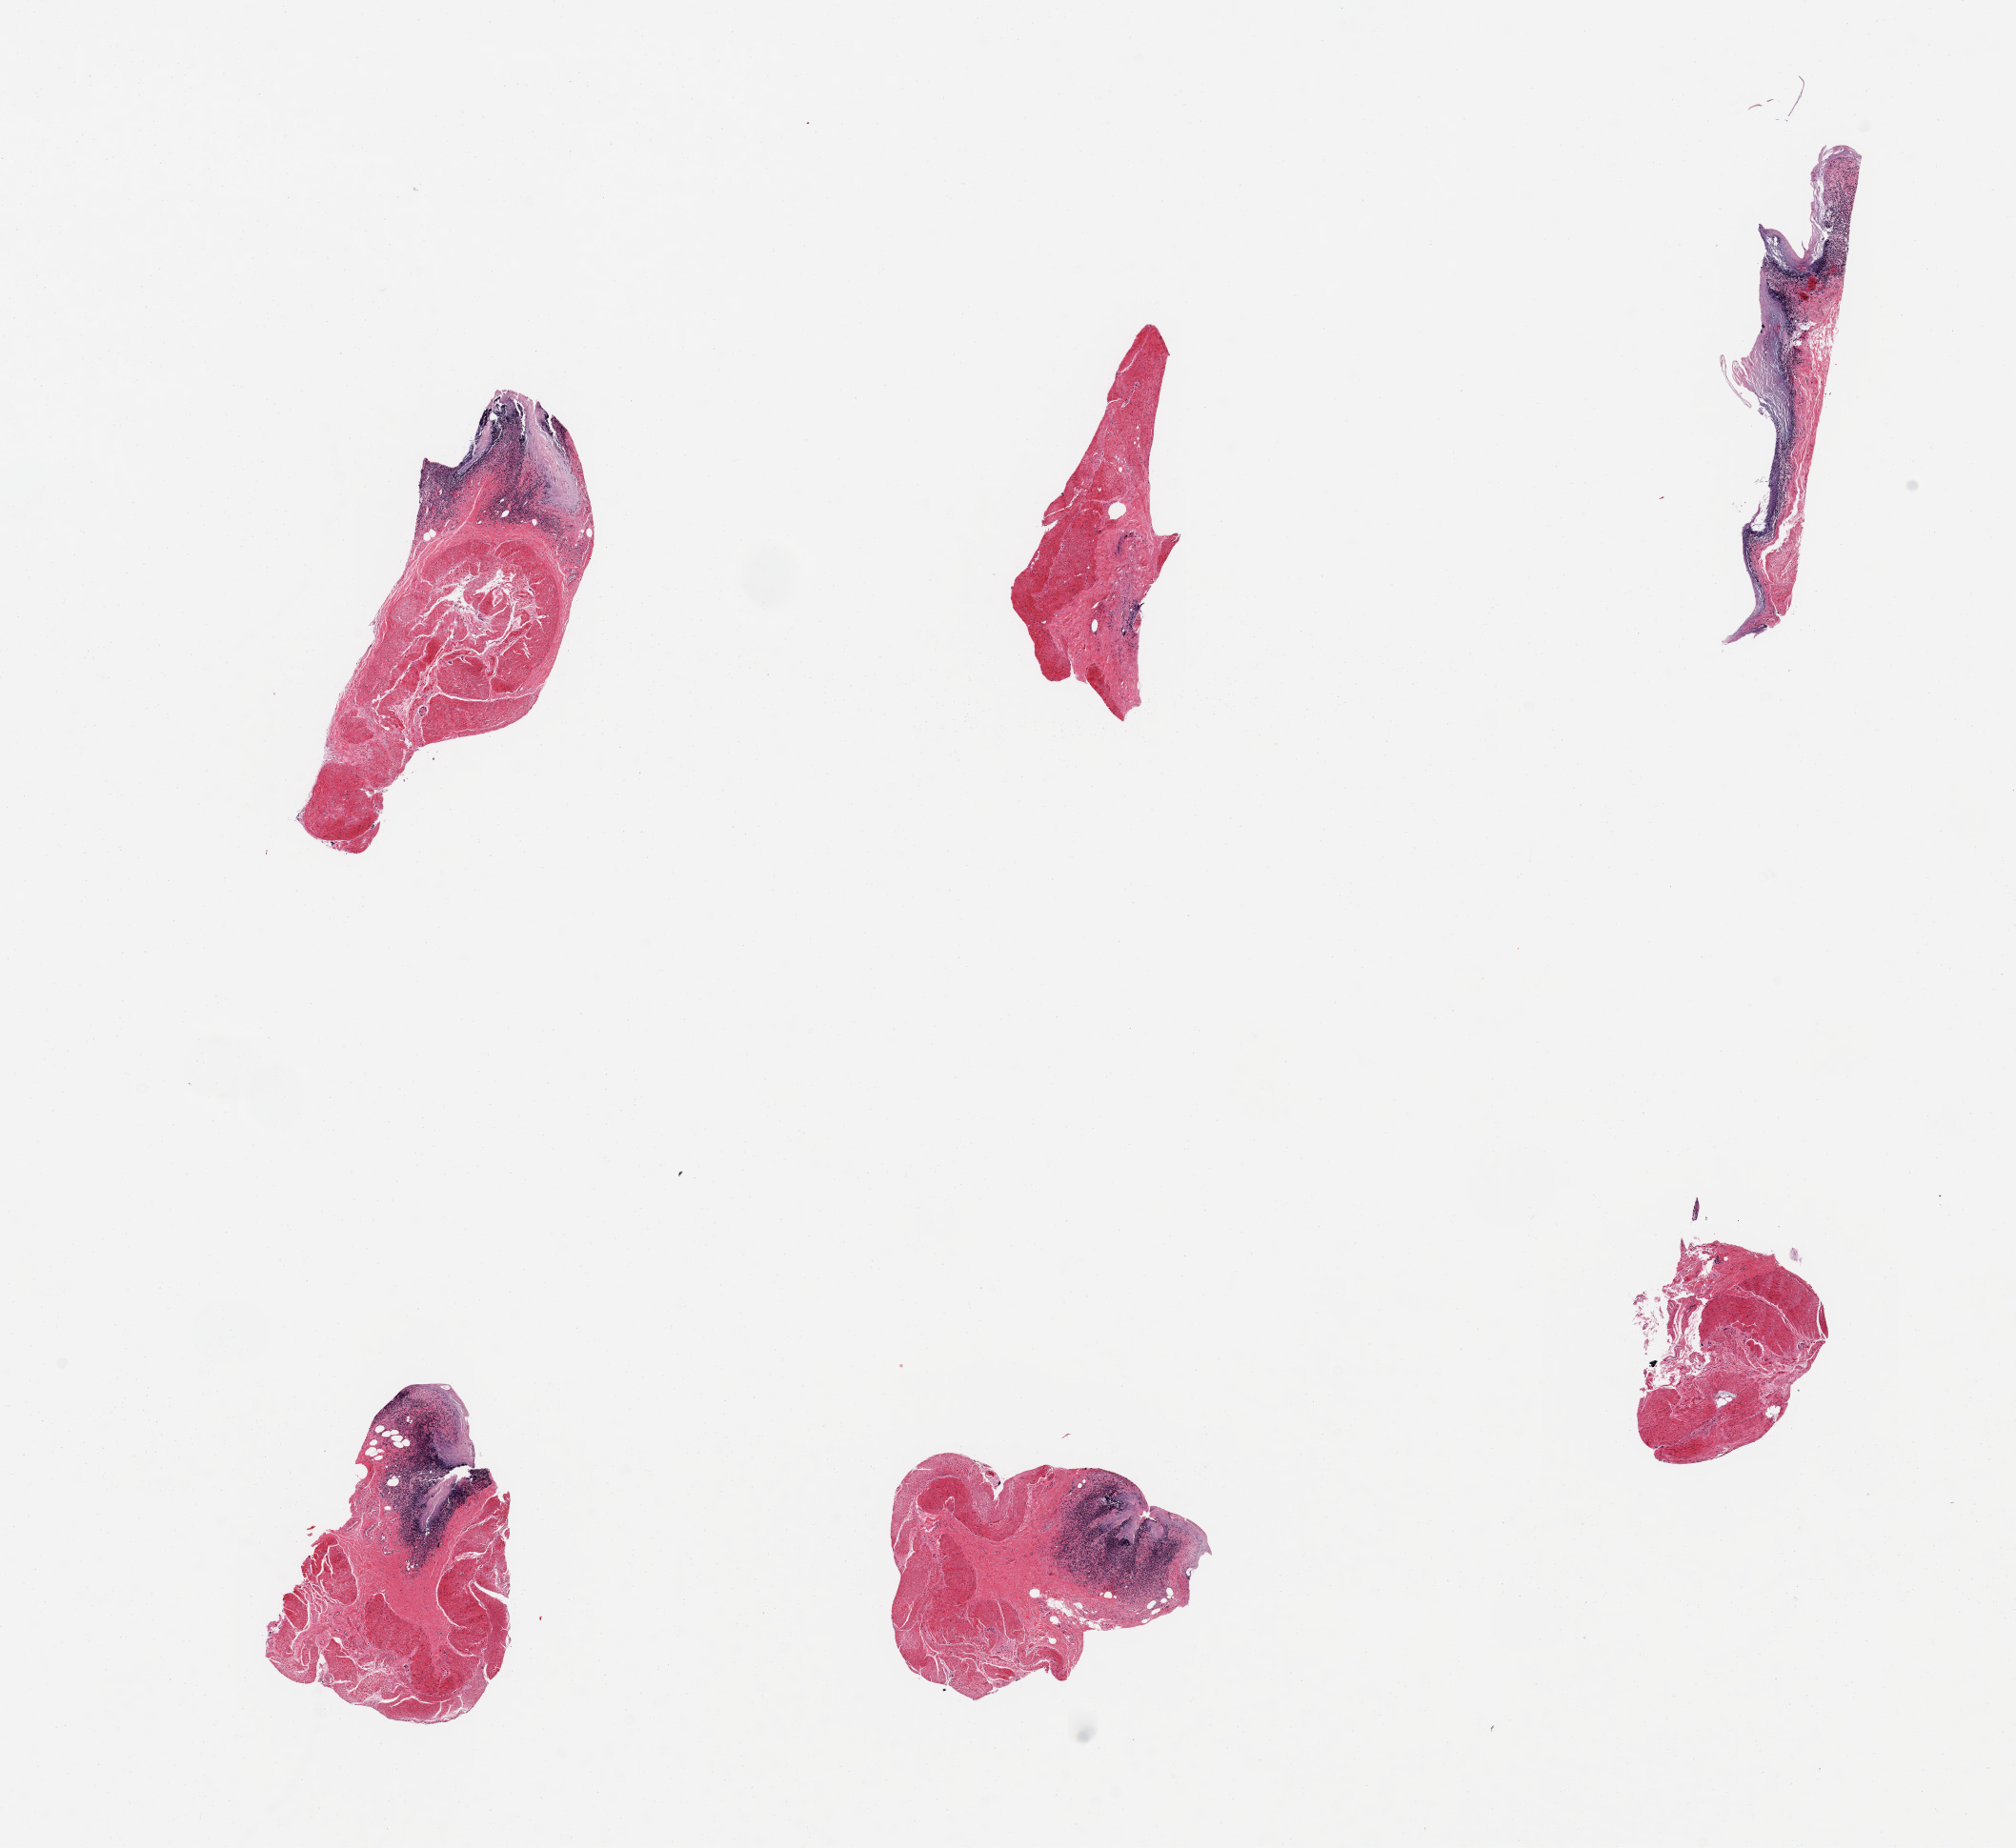
Digitized H&E-stained section — whole scanned area (about 16.7 x 15.3 mm) shown as a low-resolution overview; PAXgene-fixed paraffin-embedded (PFPE) section; sampled site (target tissue): ileum; donor tissue sample.
Review note (as recorded): 6 pieces, mucosa autolyzed, lymphoid aggregates are ~15-20% total.